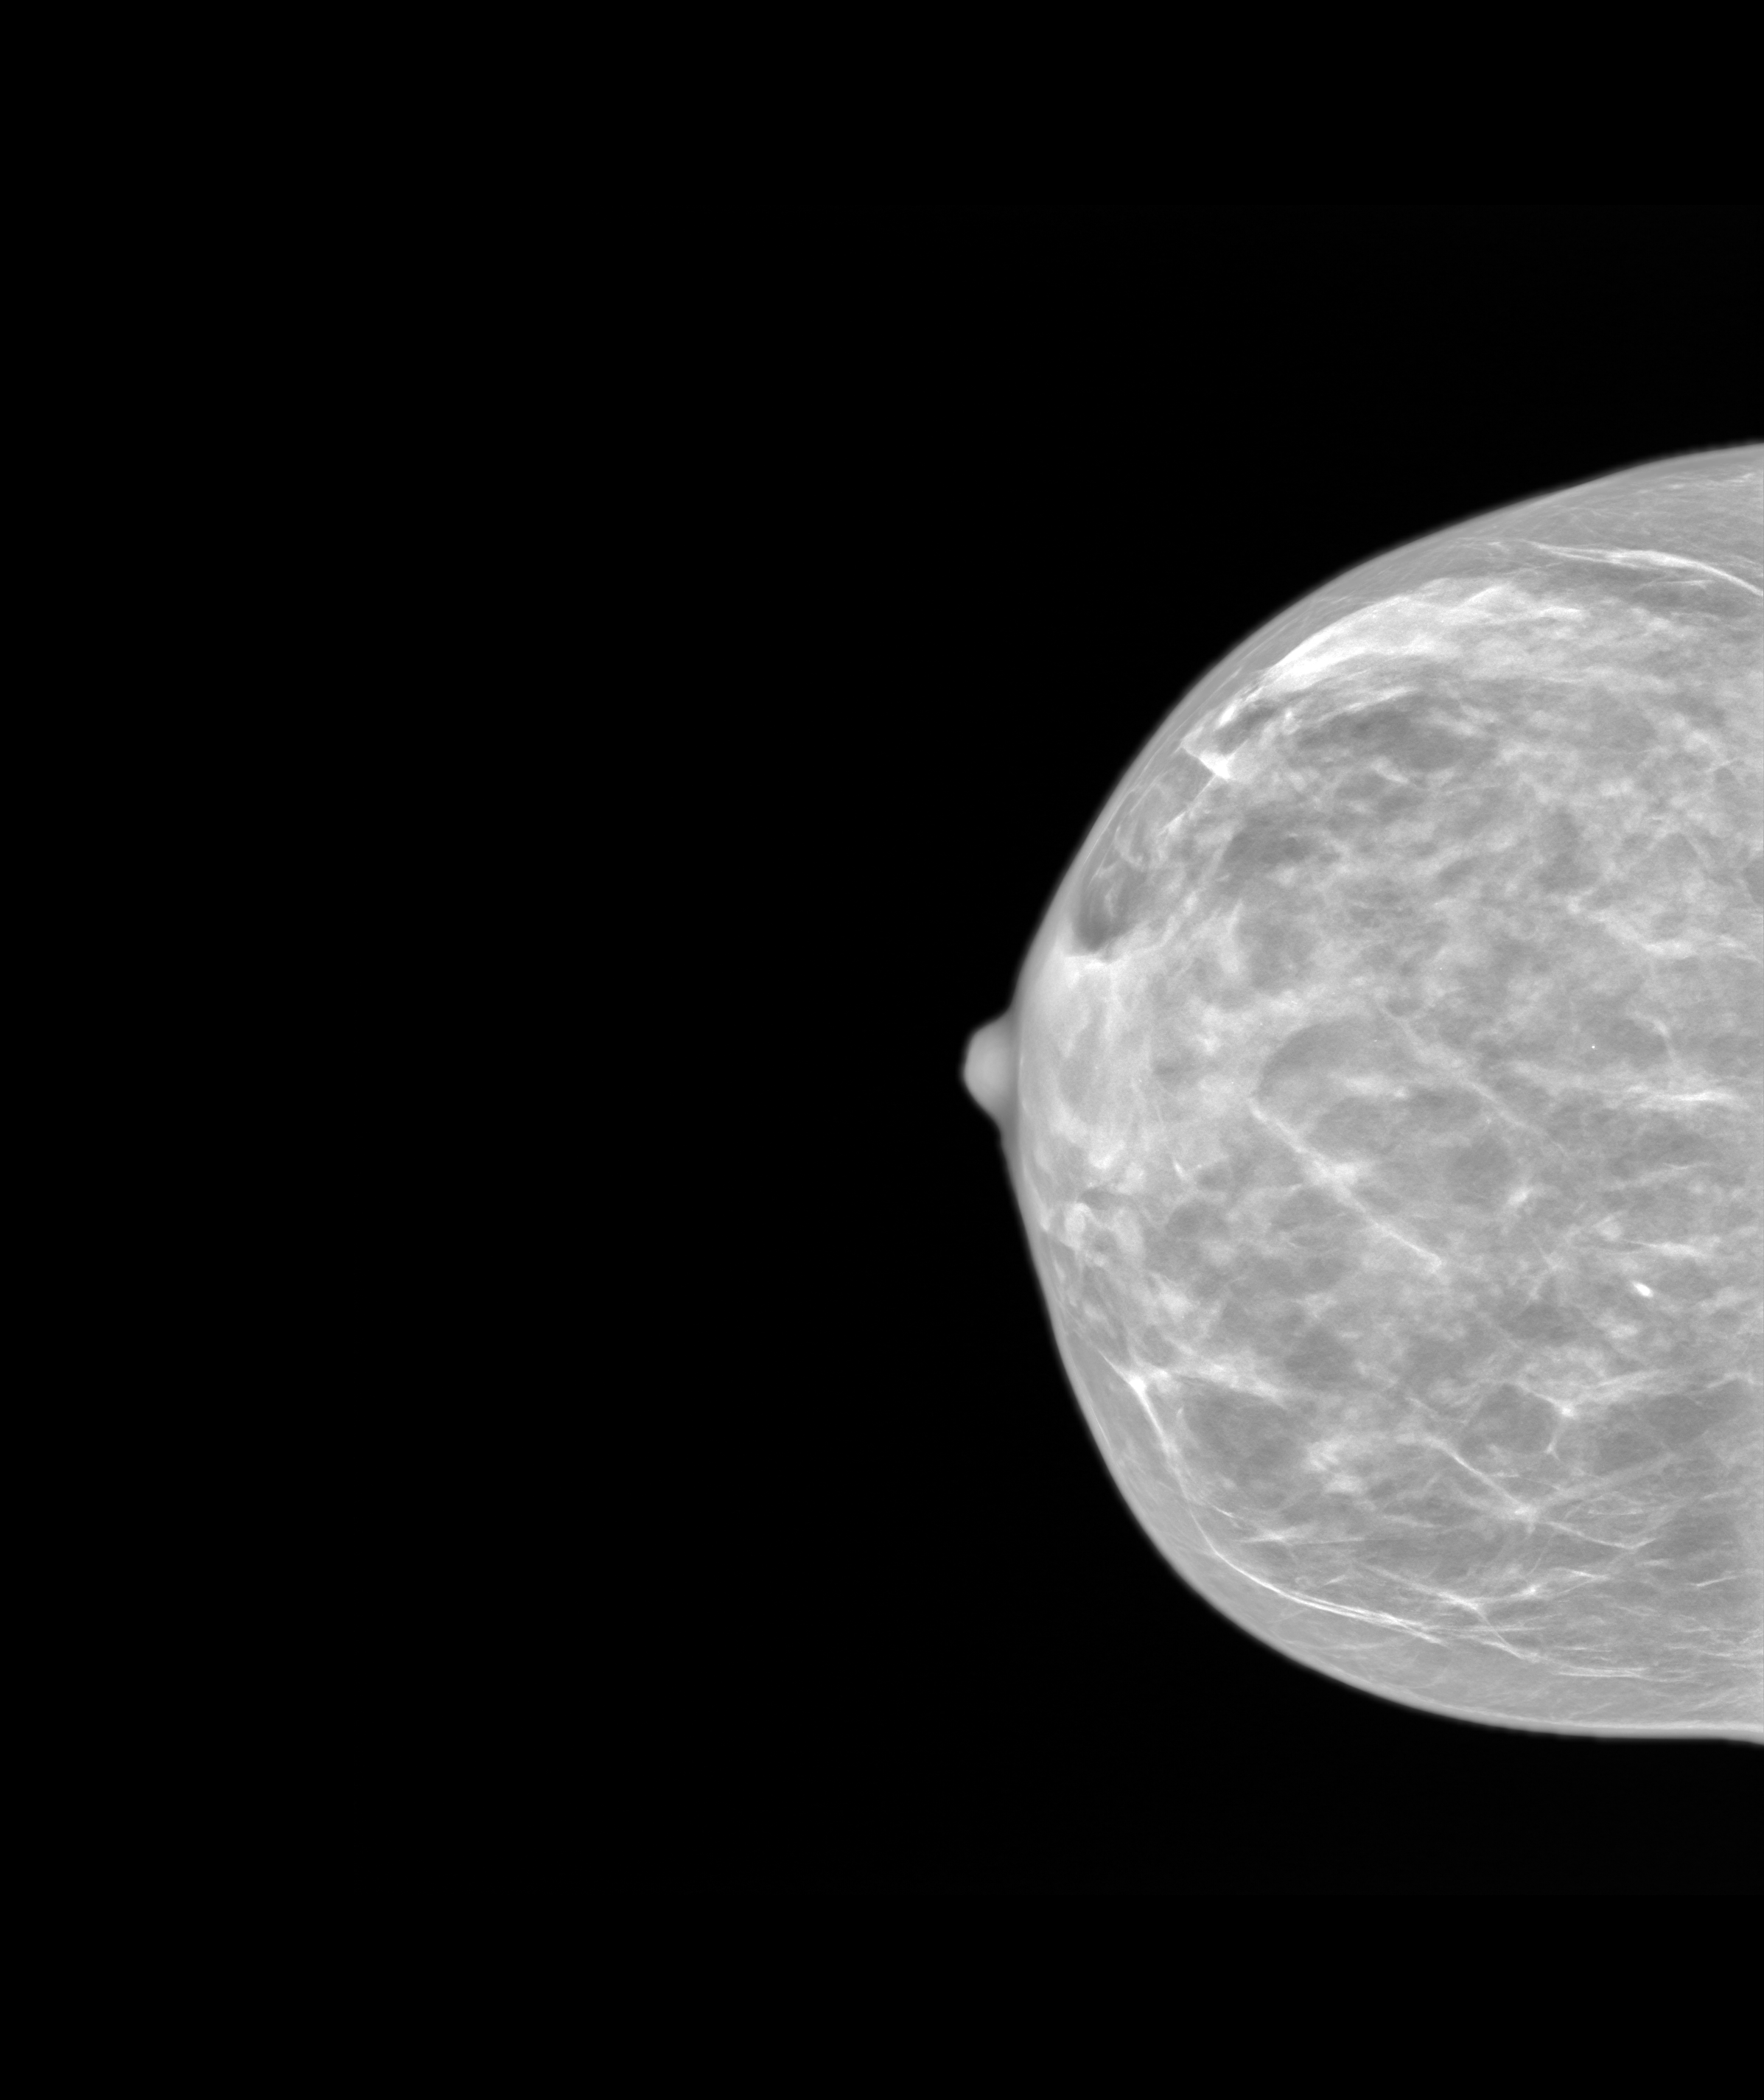
Synthetic 2-D view generated from a tomosynthesis acquisition (not an FFDM exposure), right breast, cranio-caudal projection, screening examination, system: SenoIris_1SP1.1(421). Patient aged 47 years (female).
Breast density at the screening exam (both breasts): heterogeneously dense (BI-RADS density category c). Final BI-RADS category for the screening round (tomosynthesis exam, both breasts): category 3. Recall: recalled for additional imaging after this screen.